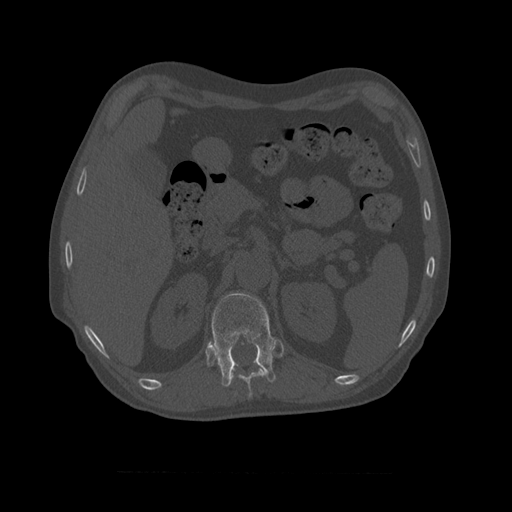
CT including the spine, one axial slice. Slice 383 of 450 in the series (ordered by position). 120 kVp. Bone window (W 1800 / L 400 HU). 512 × 512 image matrix, field of view 405 × 405 mm. Patient age 75 years. Case-level facts recorded for this patient, not image findings: primary cancer: prostate.
Structures marked on this image (semi-automatic segmentation, software-assisted and operator-edited):
- T10 vertebra: bounding box [x1, y1, x2, y2] px = [230, 368, 266, 398]
- T11 vertebra: [209, 292, 276, 387]